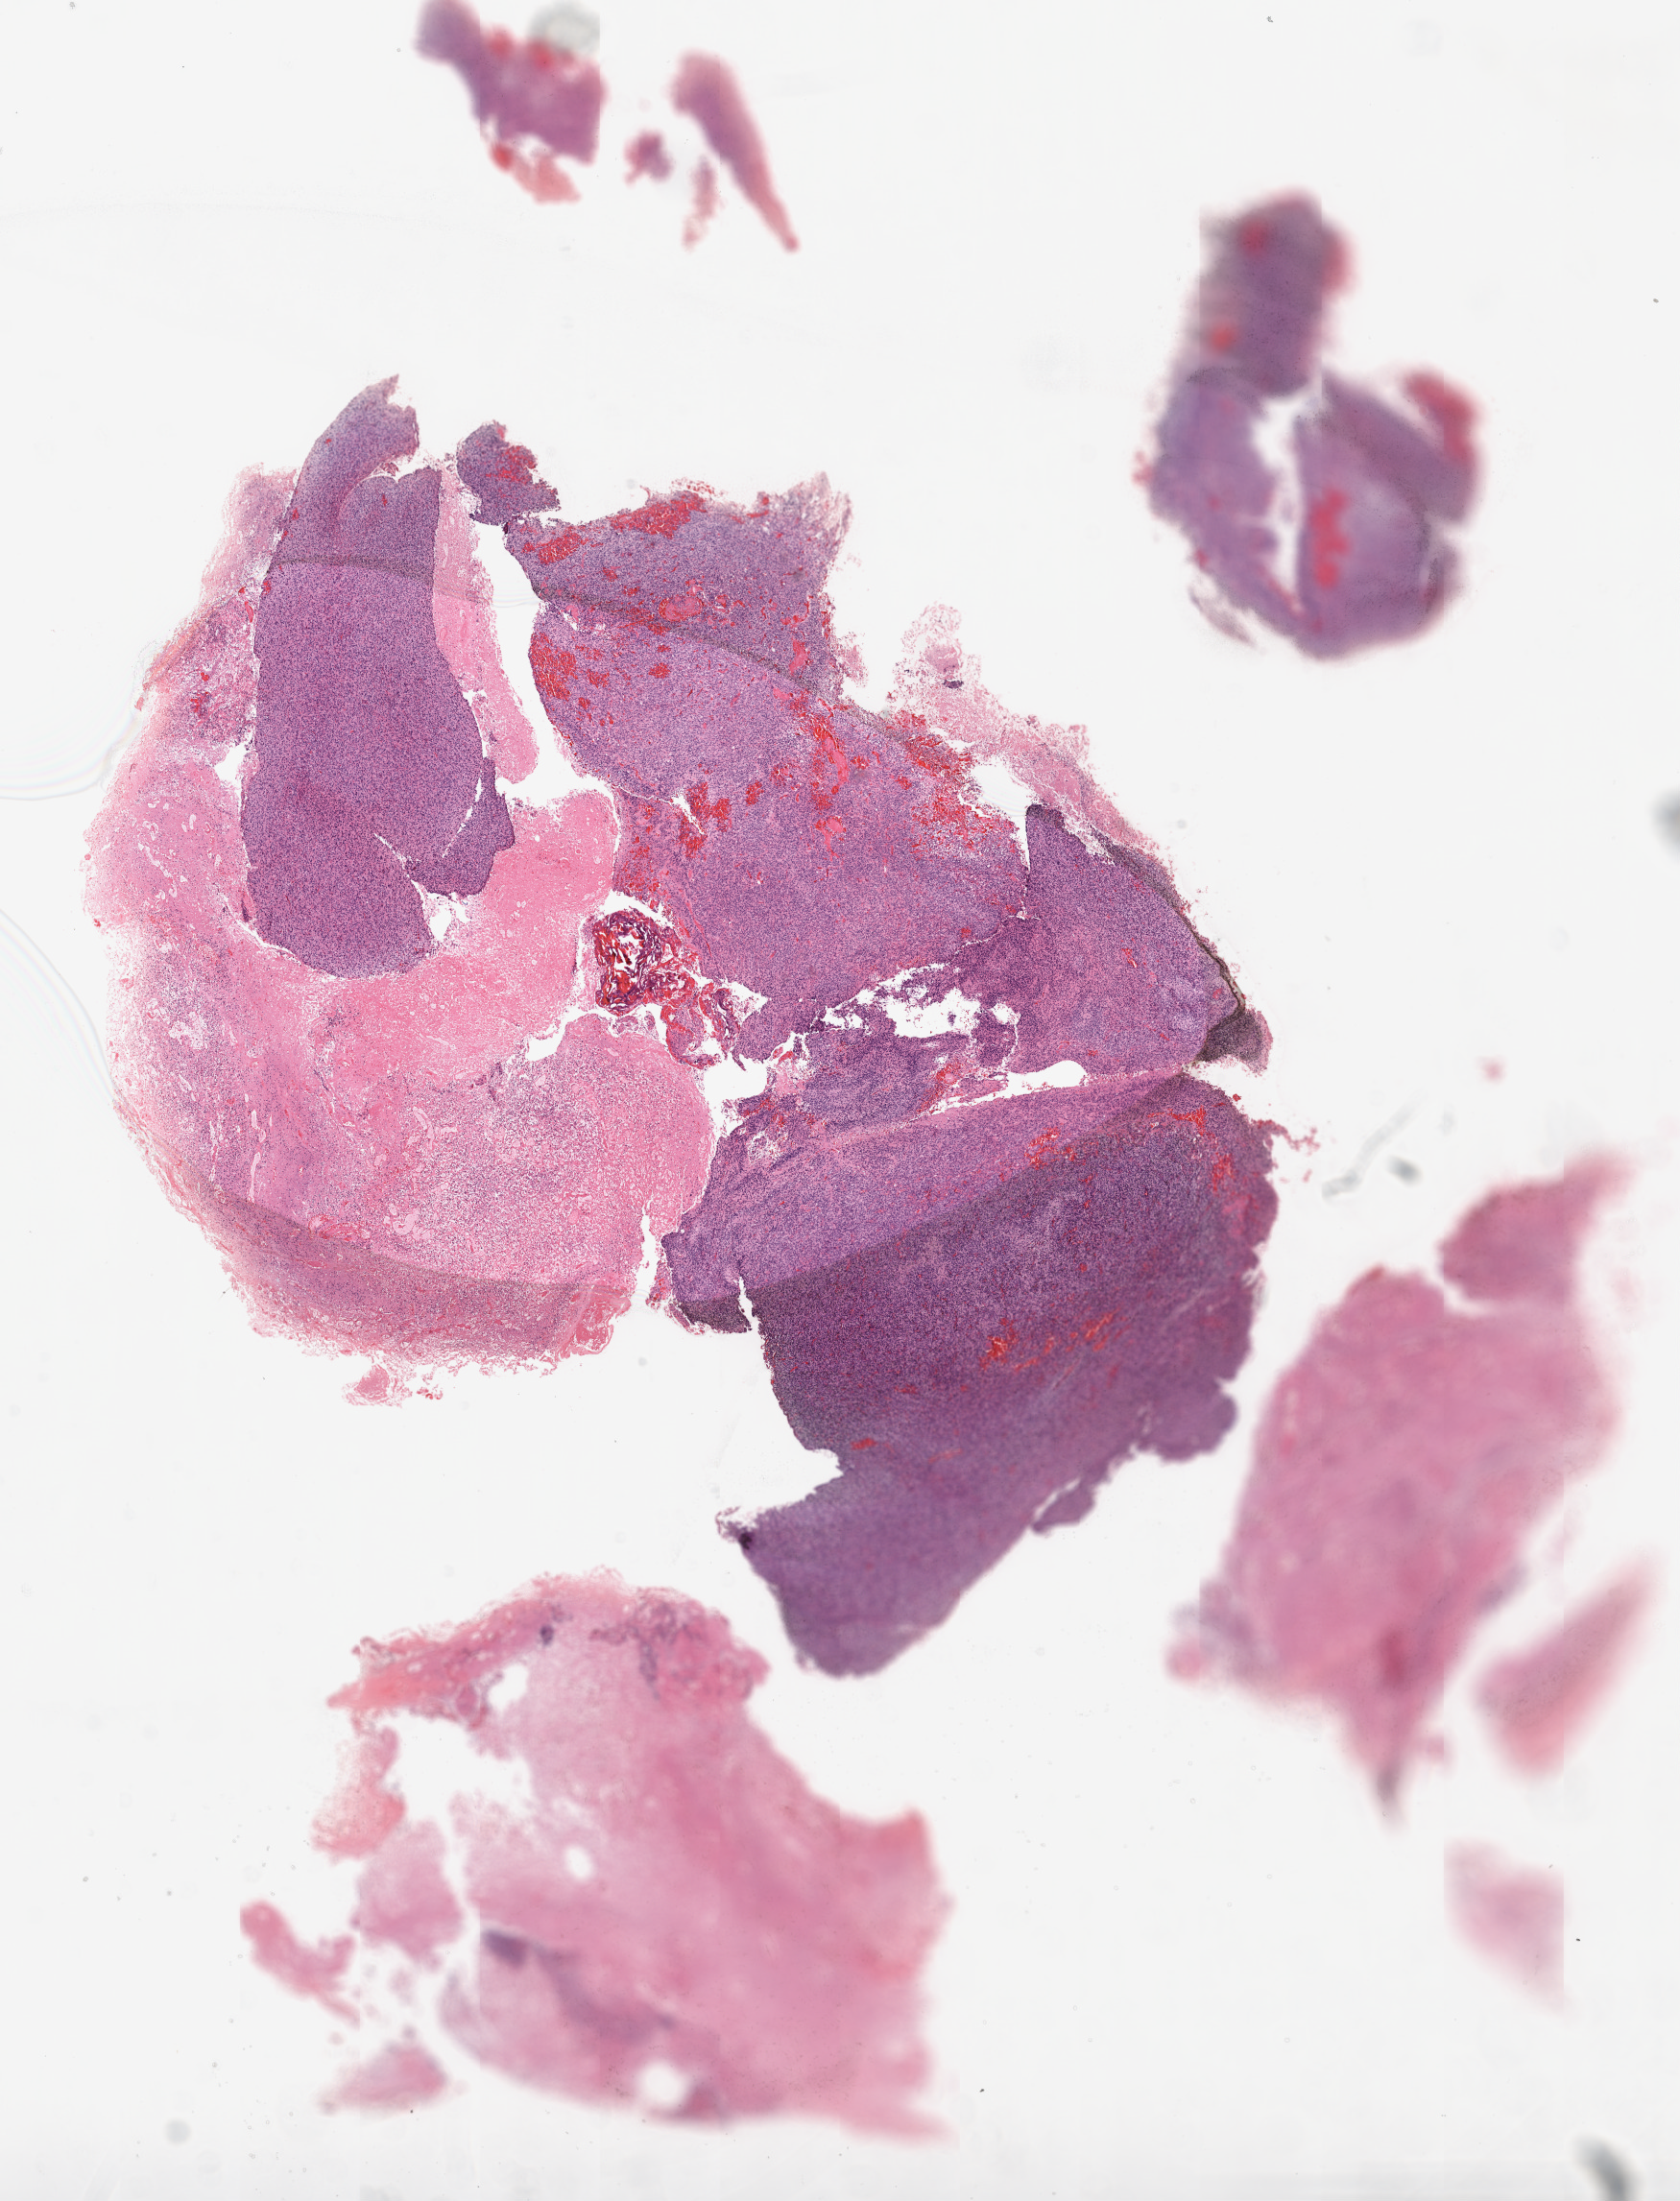
Digitized Hematoxylin and eosin (H&E) stained tissue section (whole slide), whole scanned area (about 14.0 x 18.4 mm, slide scanned at 20x) shown as a low-resolution overview; FFPE section; primary tumour sample from the brain. Patient: female, age at initial diagnosis 50 years.
Diagnosis: Glioblastoma.